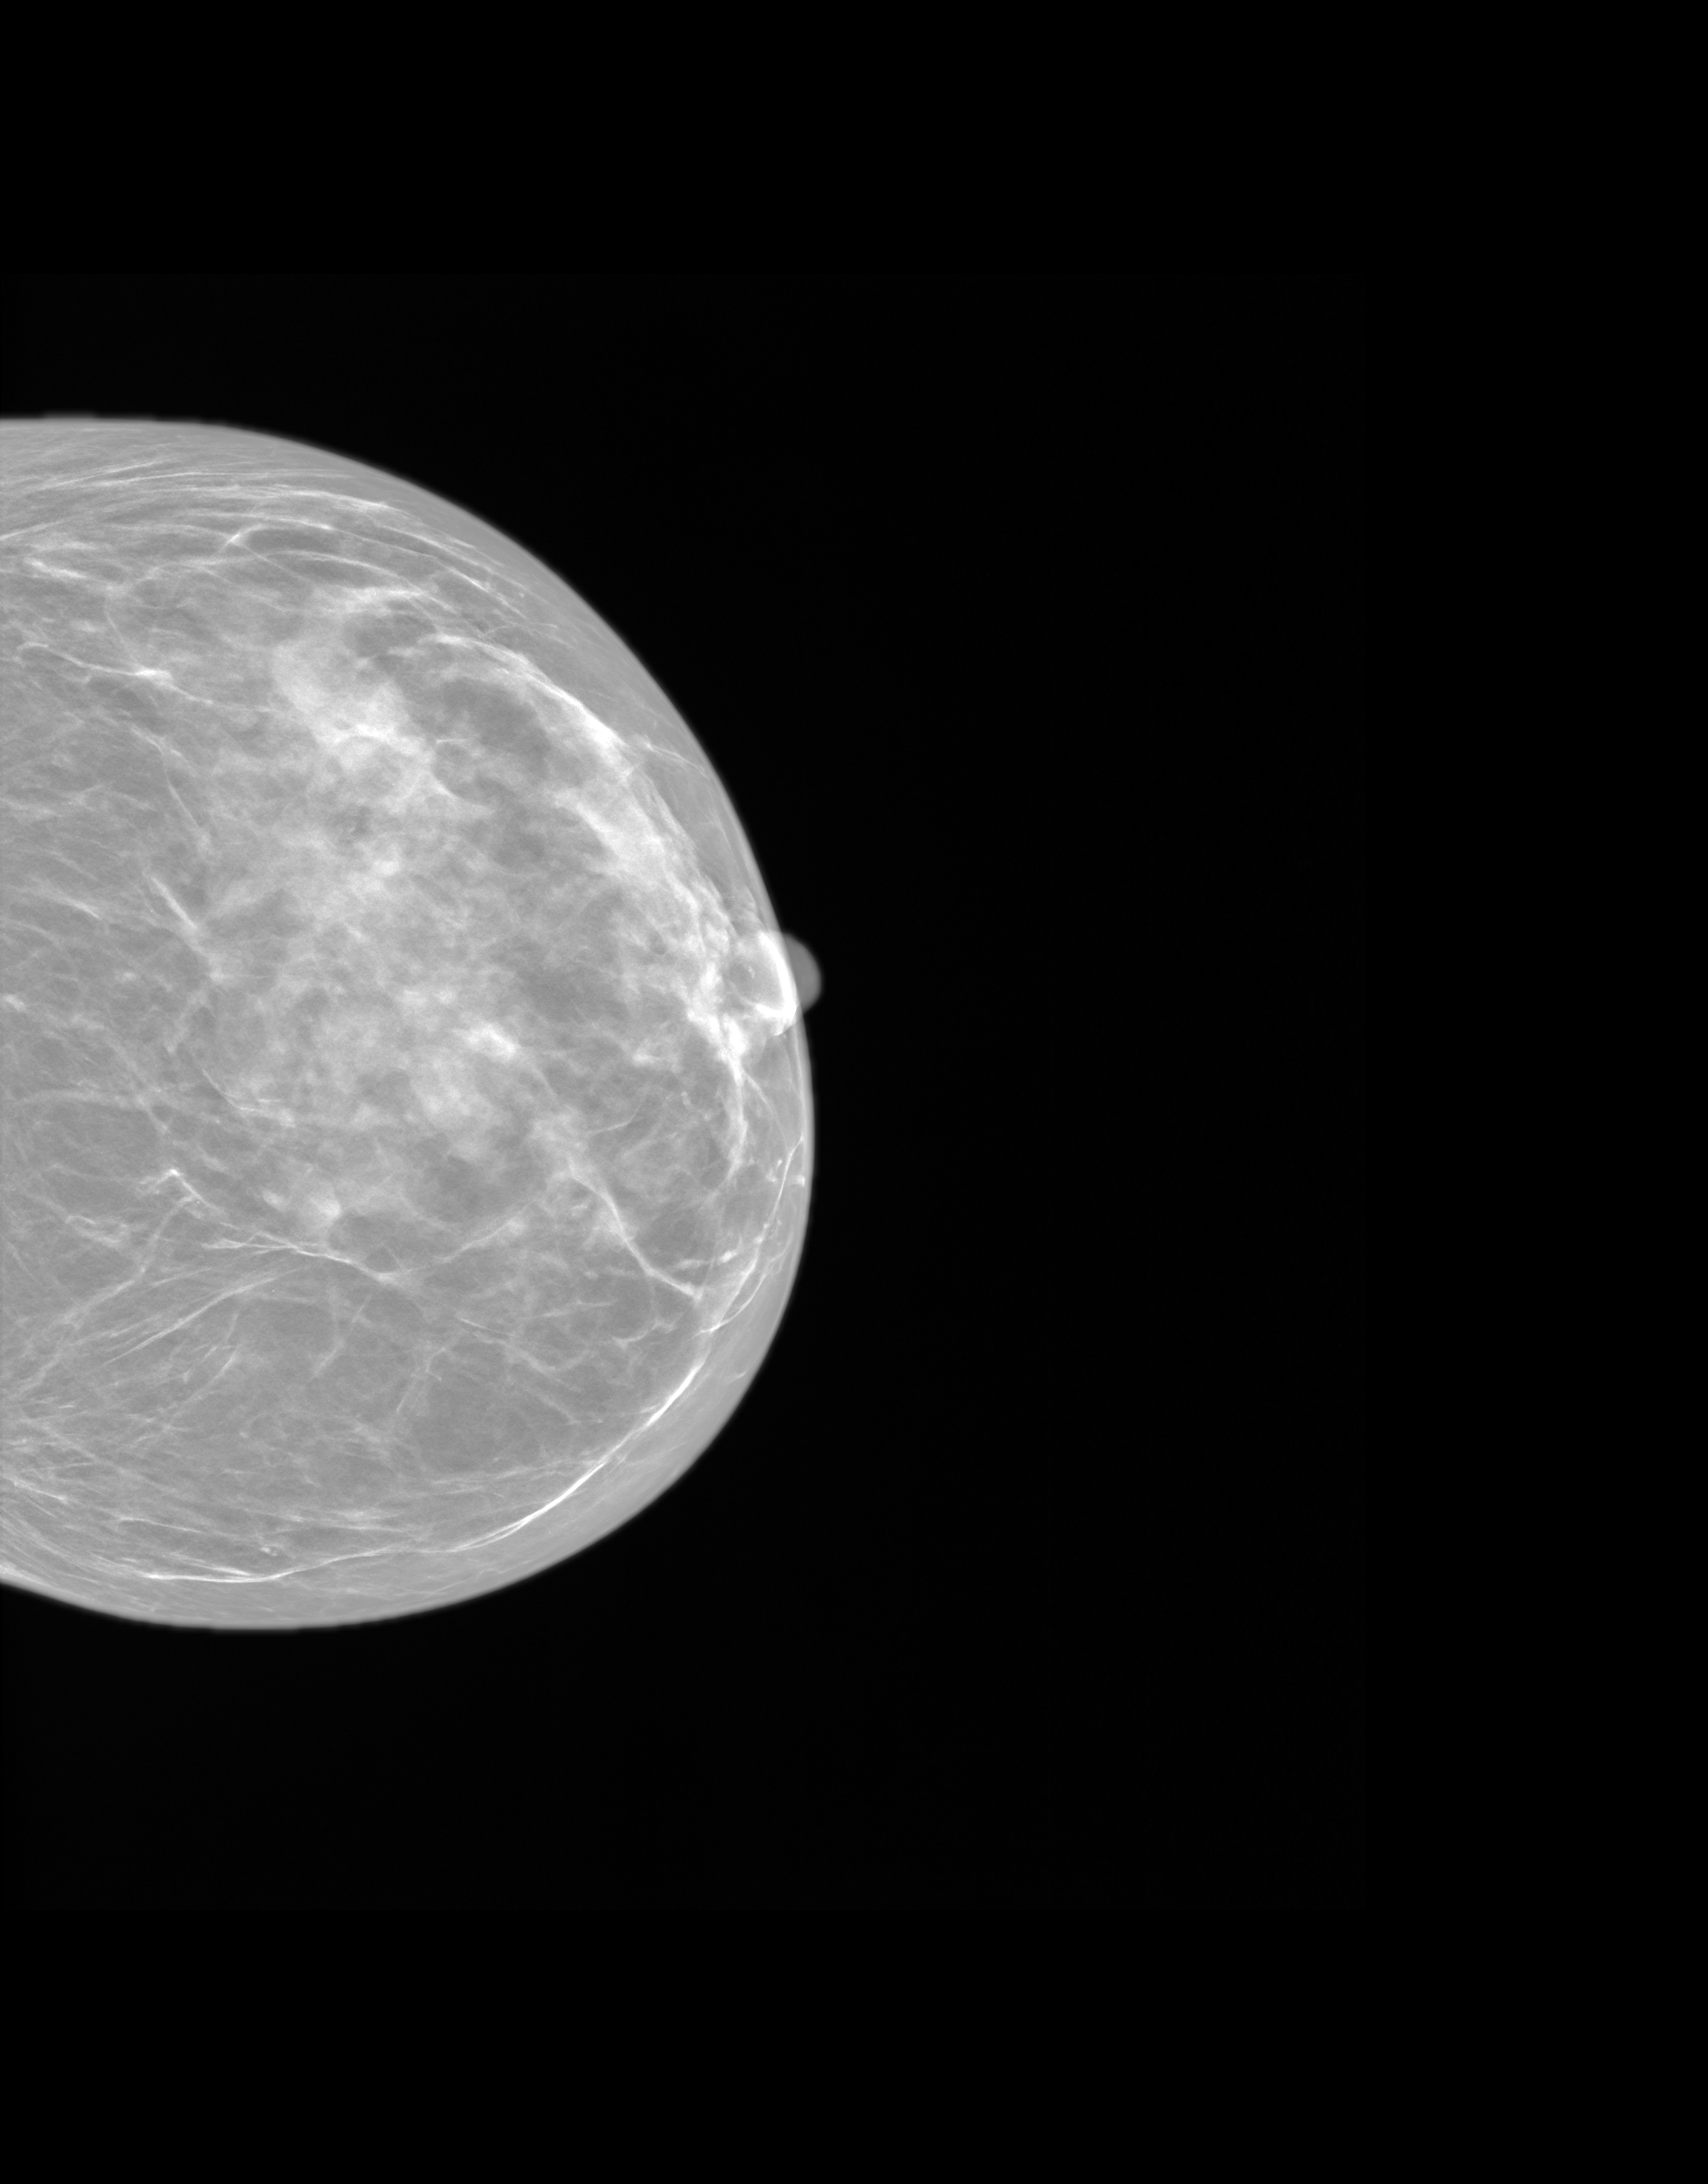
Synthesized 2-D mammogram reconstructed from digital breast tomosynthesis, left breast, cranio-caudal projection, screening examination. Female patient, age 56 years.
Breast density at the screening exam (both breasts): heterogeneously dense (BI-RADS density category c). Final BI-RADS assessment for this screening round (tomosynthesis exam, both breasts): category 1. Recall: no recall after this screen.